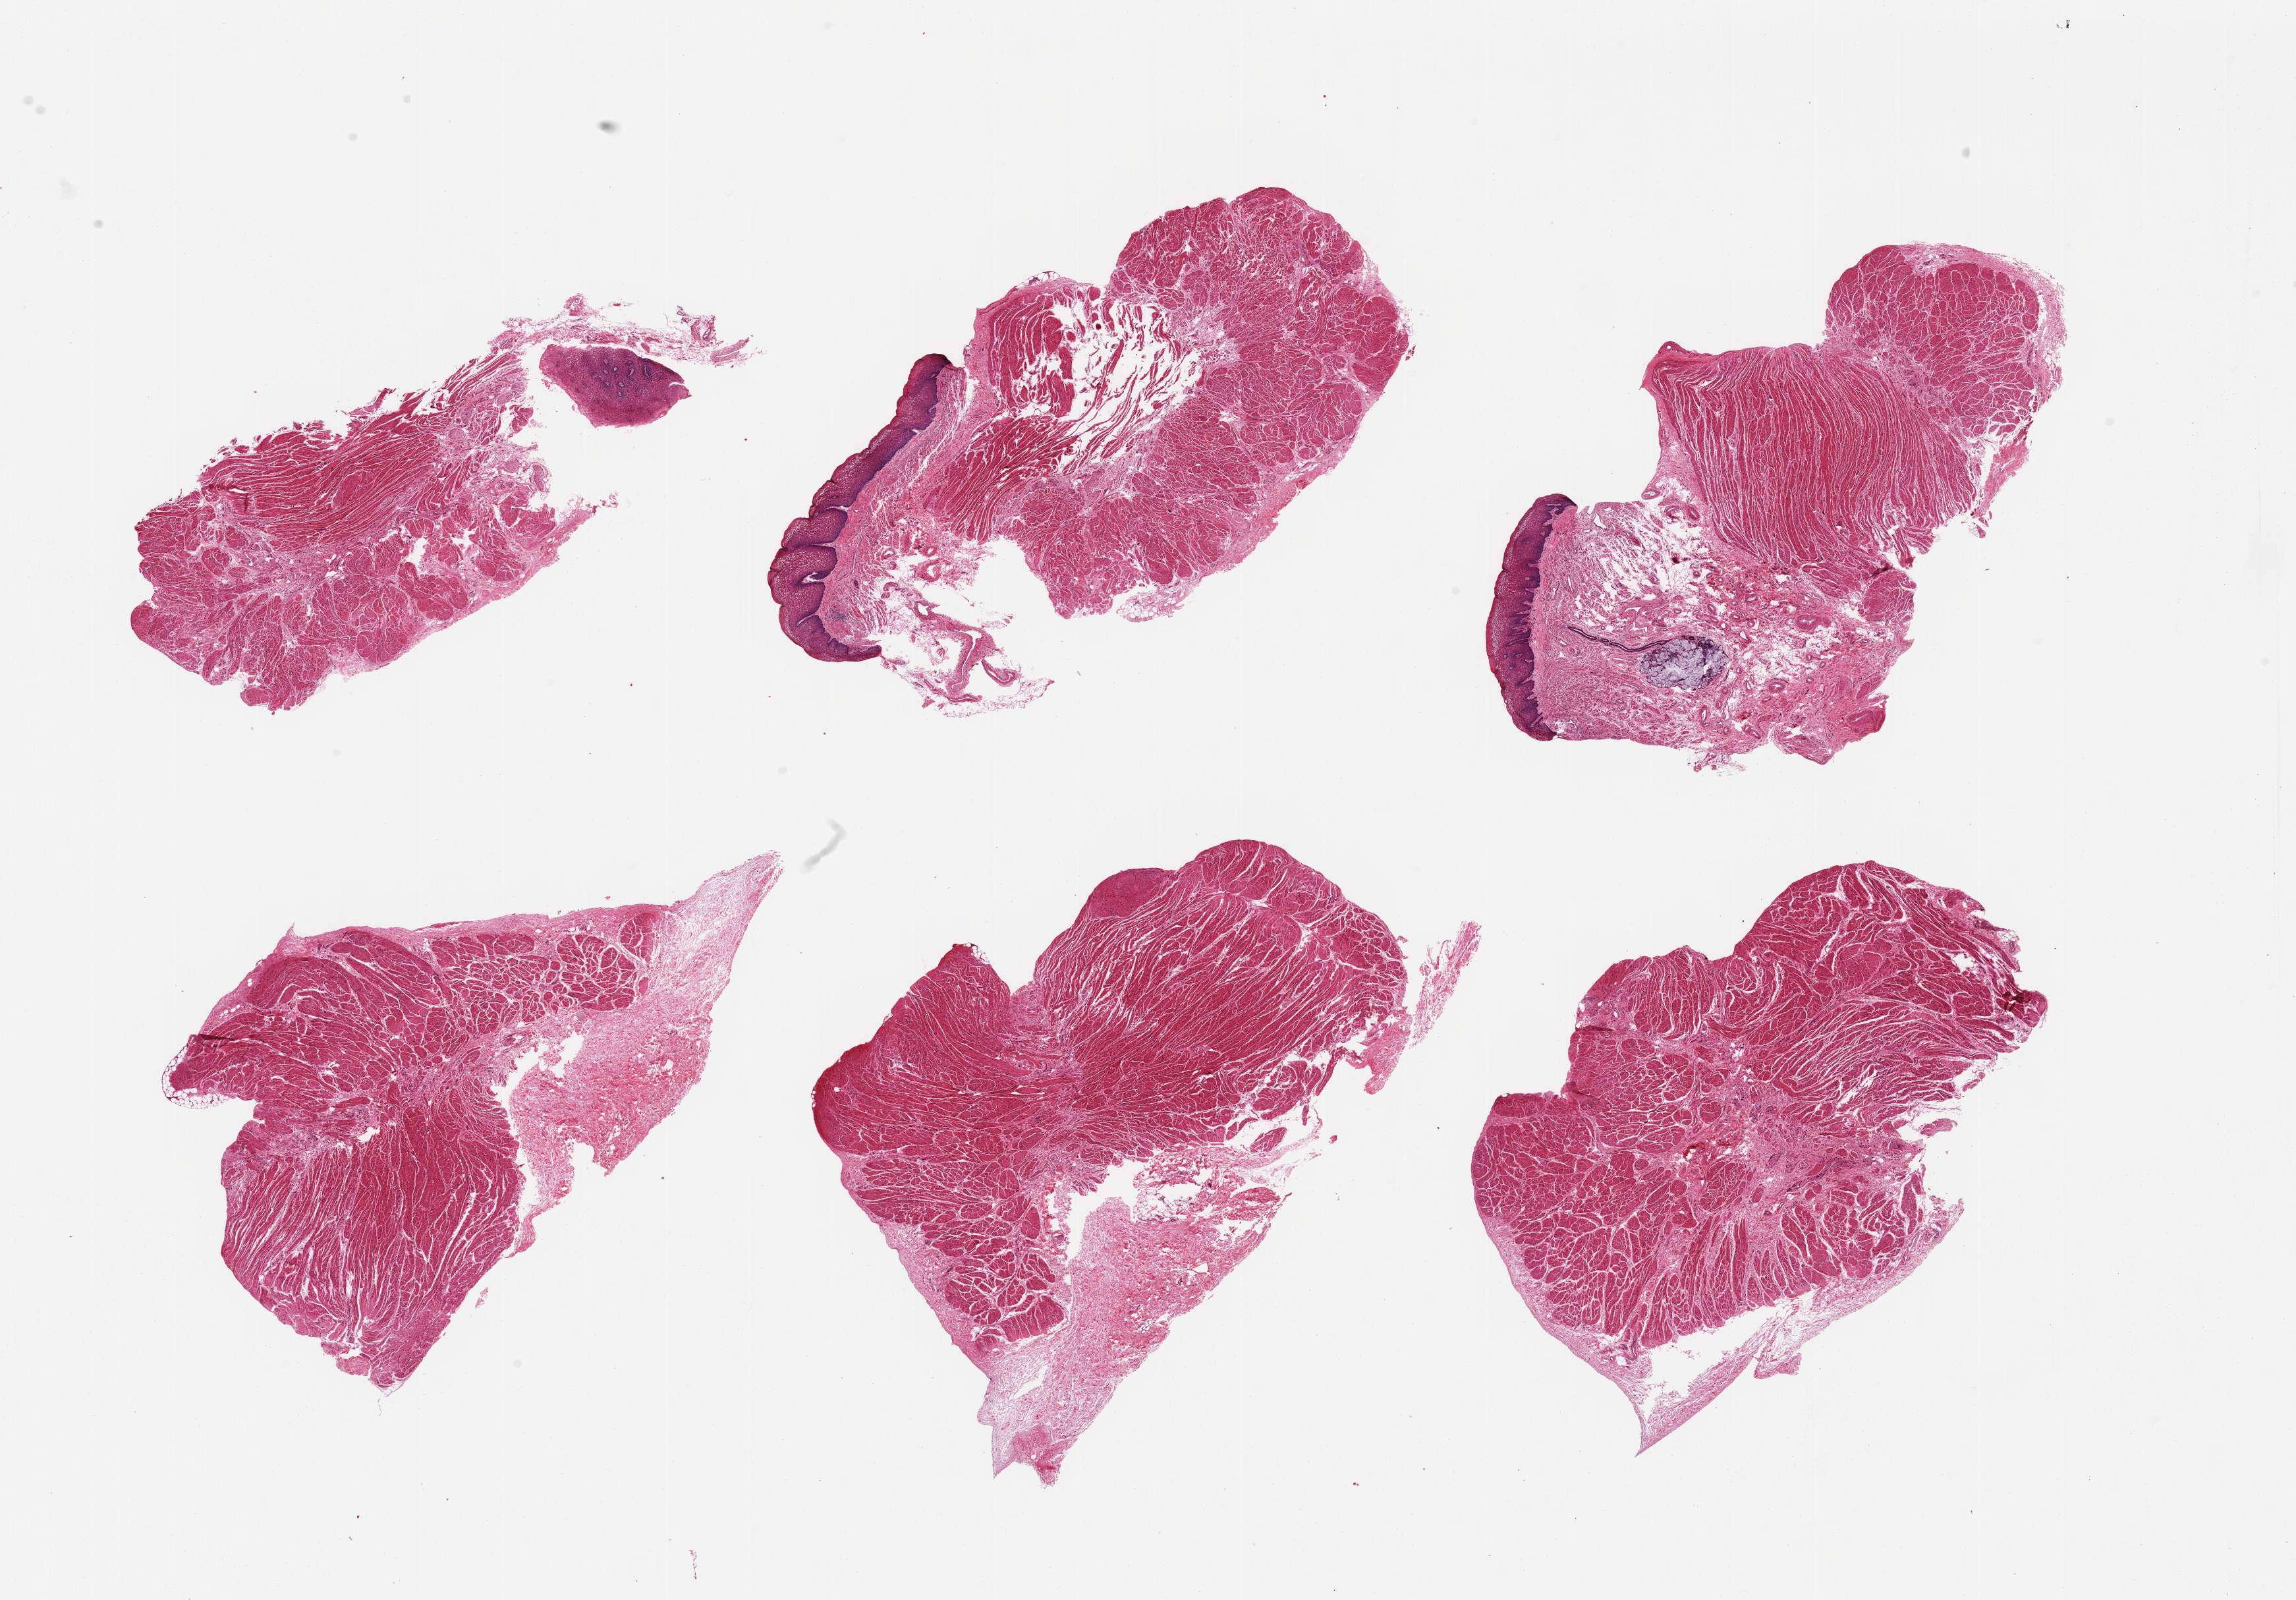
Digitized hematoxylin and eosin (H&E)-stained section, brightfield — shown as a low-resolution overview of the whole scanned area (about 27.6 x 19.2 mm); PAXgene-fixed paraffin-embedded (PFPE) section; section of gastroesophageal junction (target tissue); tissue donor sample. Male donor.
Review note (as recorded): 6 pieces, confirmed target muscularis, trace 'contaminant' squamous mucosa.